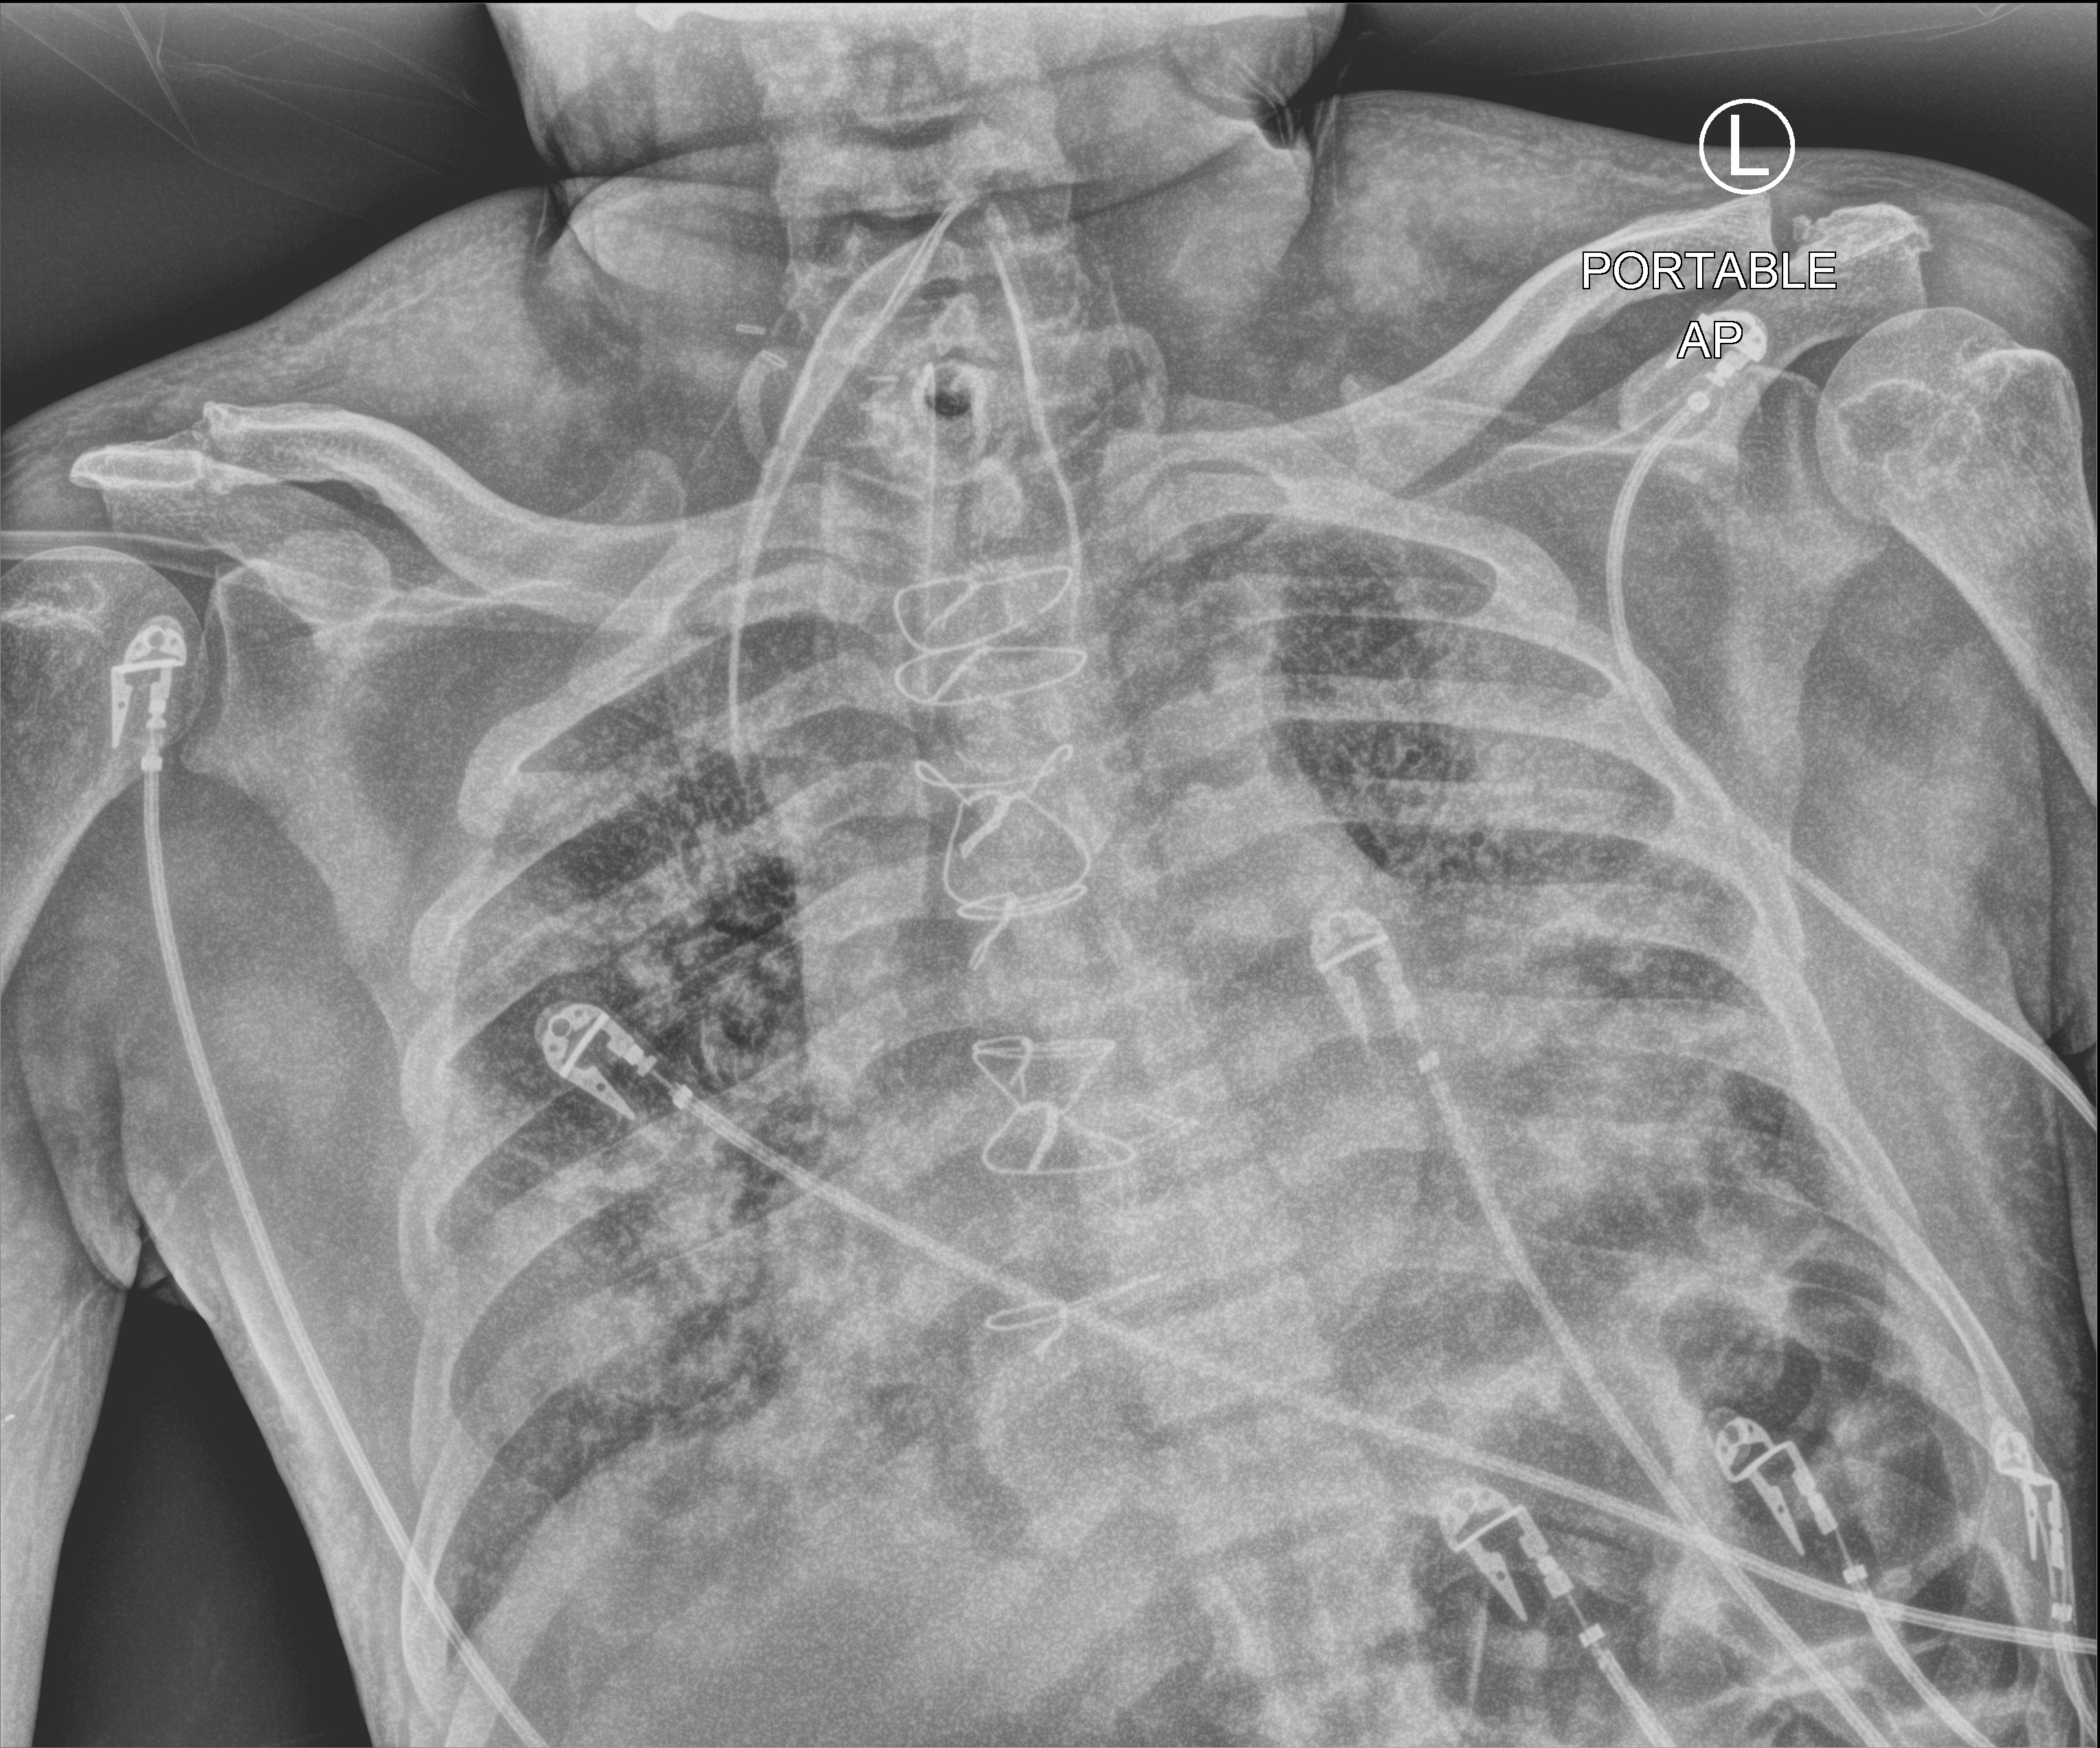
Bedside chest radiograph (computed radiography); anteroposterior (AP) projection. Male patient hospitalised with COVID-19, age 60–74 years.
From the hospital-stay record, not from the radiograph (when in the stay this image was taken is not recorded): admitted to intensive care during this hospital stay: yes; length of hospital stay: 50 days; mechanically ventilated during this hospital stay: yes.